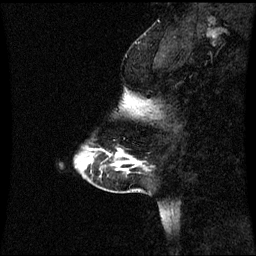
Breast MRI (dynamic contrast-enhanced), one sagittal slice; slice 12 of 60 in the series (ordered by position); dynamic contrast-enhanced series, image 2 of 3 at this slice position (ordered by acquisition); 1.5 T; TE 4.2 ms, TR 8.9 ms; 2 mm slice thickness; 256 × 256 image matrix. Female patient, age 43 years. From the clinical record (not read from this slice): setting: breast cancer imaged before/during neoadjuvant chemotherapy; receptor status: HR-positive, HER2-negative.
Structures marked on this image (semi-automatic segmentation, software-assisted and operator-edited):
- analysis volume of interest (the breast-tissue region the enhancement analysis was run in; not a lesion): bounding box [x1, y1, x2, y2] px = [84, 116, 144, 171]
- tumour enhancement mask (voxels above the 70 % enhancement threshold inside the analysis volume of interest): [116, 150, 123, 157]